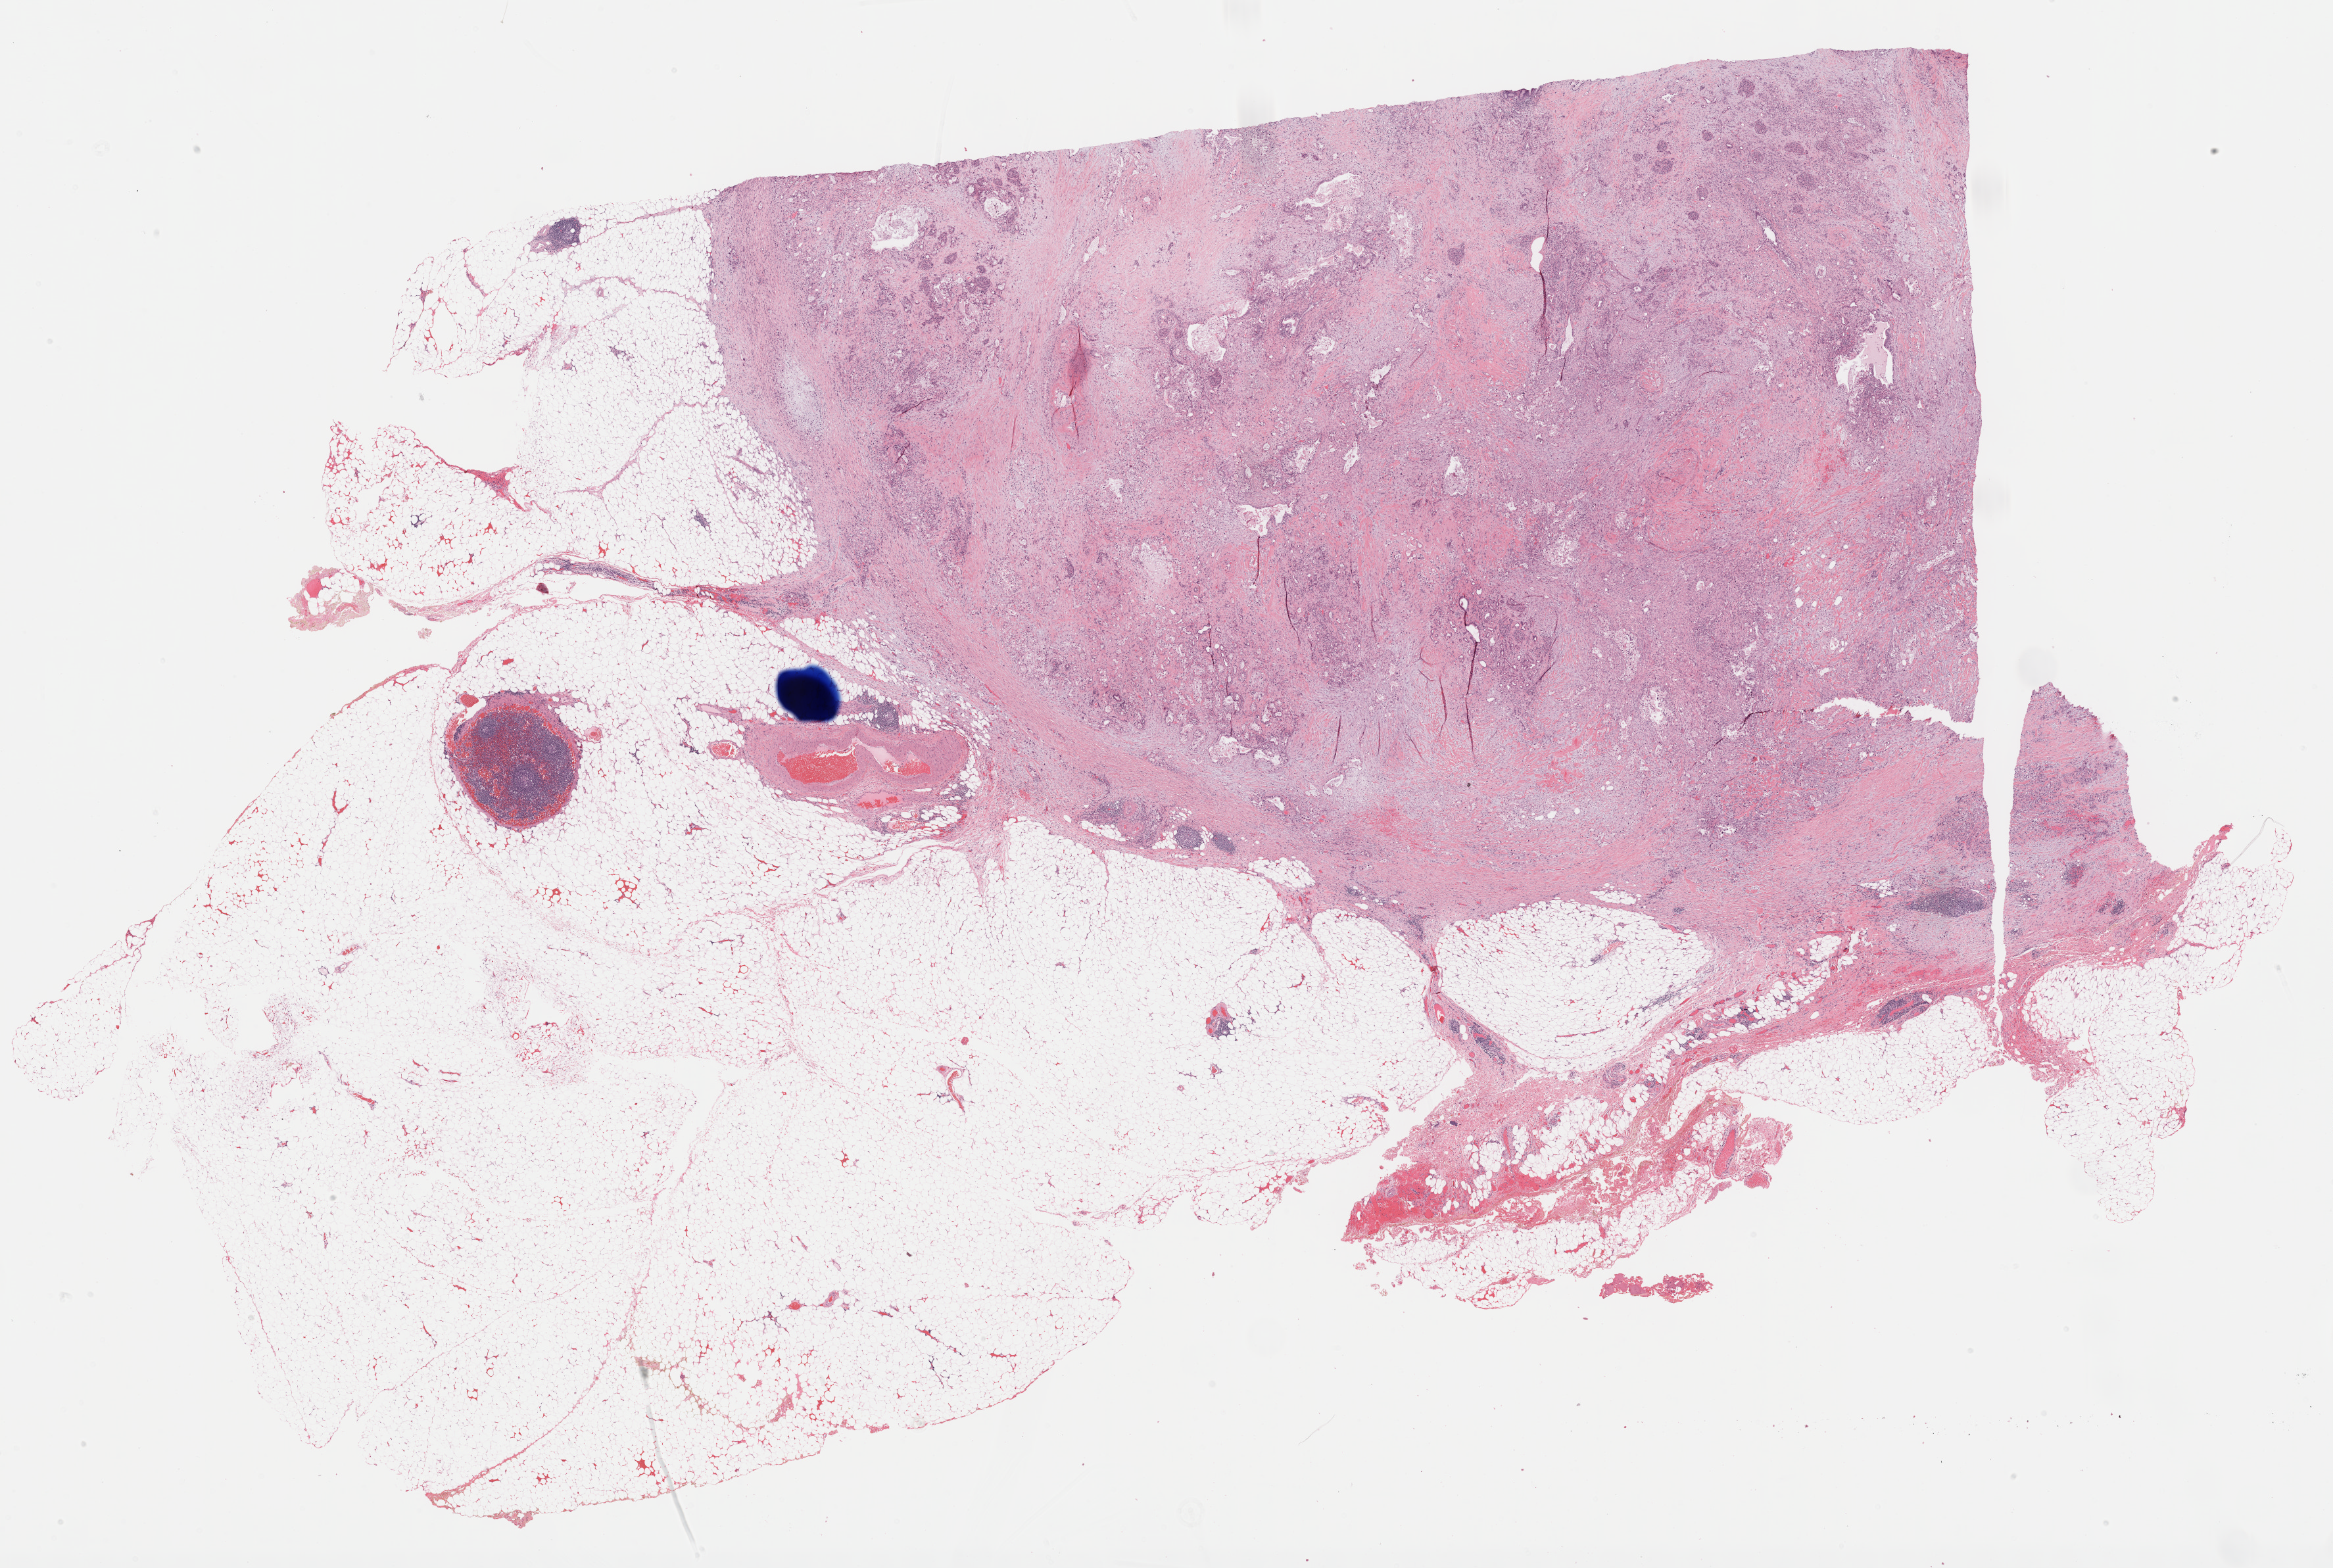
H&E whole-slide image — whole scanned area (about 28.7 x 19.3 mm) shown as a low-resolution overview, formalin-fixed paraffin-embedded (FFPE) diagnostic section, sample: primary tumour, pancreas. Patient: male, age at initial diagnosis 73 years. Histologic grade: G3 (poorly differentiated).
- AJCC pathologic stage: IB
- lymph nodes positive (case pathology): 0 of 11 examined
- pathologic diagnosis: Infiltrating duct carcinoma, NOS